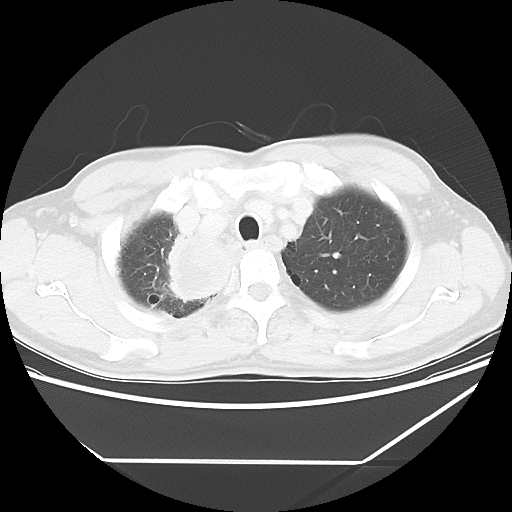
Chest CT, one axial slice. Position 51 of 60 along the scan axis. Reconstruction kernel LUNG. 120 kVp. Lung window (W 1500 / L -600 HU). 5 mm slice thickness. 512 × 512 image matrix, field of view 367 × 367 mm. Patient: male, 58 years. From the clinical record (not read from this slice): clinical TNM (as recorded): T2 N2 M0.
Outlined on this slice (bounding box drawn by a radiologist):
- lung tumour (recorded histology: squamous cell carcinoma): bounding box <154,215,237,305> (left, top, right, bottom; pixels)